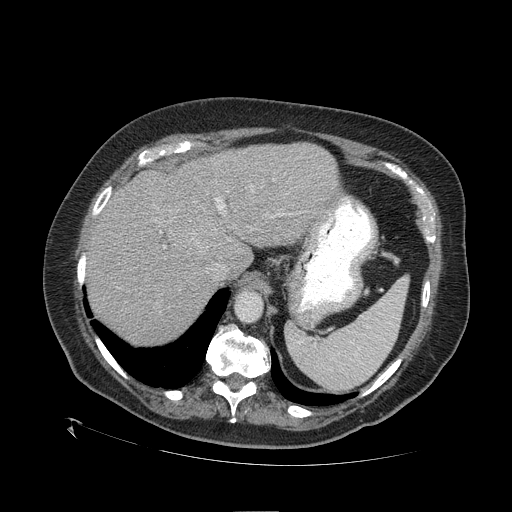
Contrast-enhanced abdominal CT (liver protocol), one axial slice. Slice 81 of 109 in the series (ordered by position). Reconstruction kernel STANDARD. One of 2 acquisitions stored at this slice position. Soft-tissue window (W 400 / L 40 HU). 2.5 mm slice thickness. 512 × 512 image matrix, field of view 460 × 460 mm. From the clinical record (not read from this slice): diagnosis: hepatocellular carcinoma (patient treated with transarterial chemoembolisation; whether this scan precedes or follows treatment is not stated here); TNM stage (as recorded): Stage-I.
Annotated regions visible in this slice (semi-automatic segmentation, software-assisted and operator-edited):
- liver parenchyma outside the tumour (the mass and vessels are separate outlines, so this box may not span the whole liver): bounding box [x1, y1, x2, y2] px = [88, 142, 340, 344]
- mass: [162, 200, 220, 254]
- liver vessels: [160, 197, 292, 248]